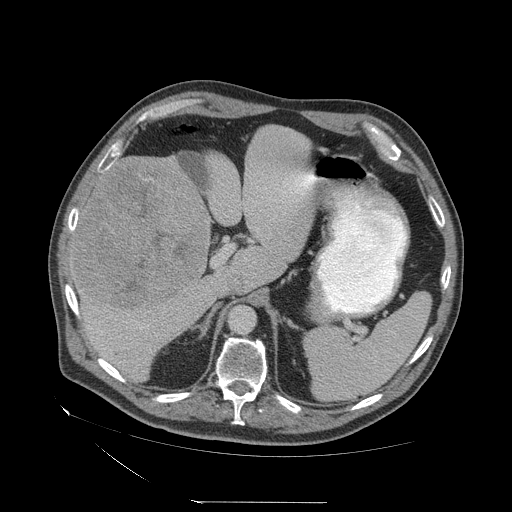
Contrast-enhanced abdominal CT (liver protocol), one axial slice; position 37 of 83 along the scan axis; 140 kVp; soft-tissue window (W 400 / L 40 HU); 512 × 512 image matrix, field of view 460 × 460 mm. From the clinical record (not read from this slice): diagnosis: hepatocellular carcinoma (patient treated with transarterial chemoembolisation; whether this scan precedes or follows treatment is not stated here); TNM stage (as recorded): Stage-I; Child-Pugh class: A; tumour differentiation: well differentiated; tumour nodularity: uninodular.
Outlined on this slice (semi-automatic segmentation, software-assisted and operator-edited):
- liver parenchyma outside the tumour (the mass and vessels are separate outlines, so this box may not span the whole liver): bounding box (x1, y1, x2, y2) in pixels: (70, 134, 312, 382)
- mass: (72, 157, 210, 310)
- liver vessels: (106, 165, 306, 329)